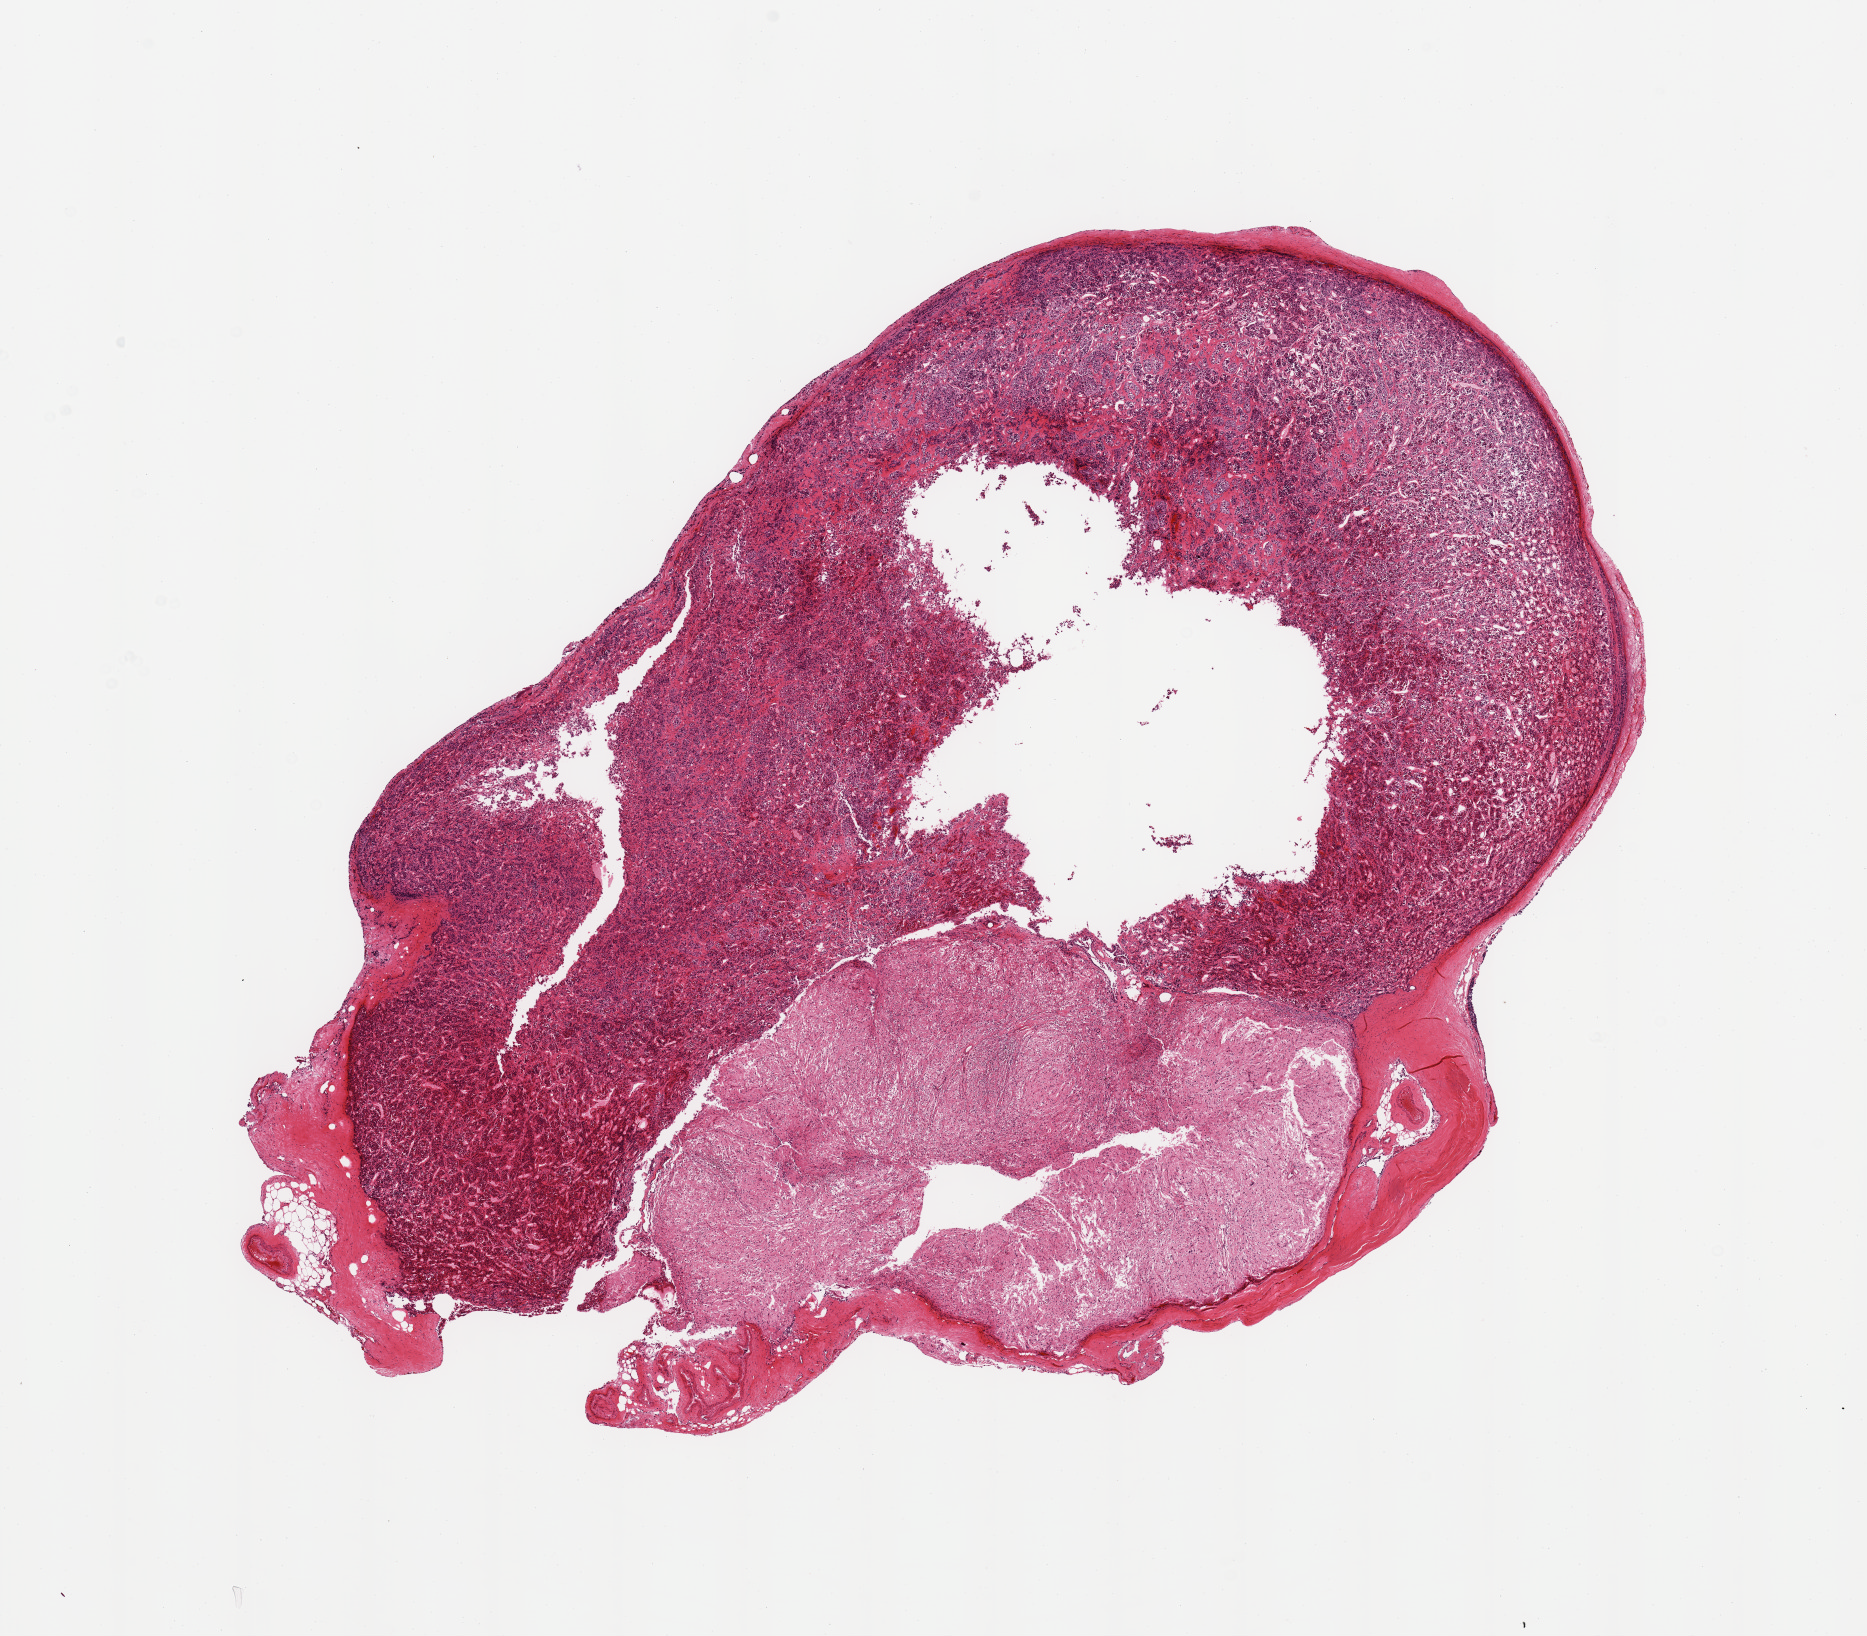
Digitized hematoxylin and eosin (H&E)-stained section, a low-resolution overview of the entire scanned area, about 14.8 x 12.9 mm (from a 20x scan). PAXgene-fixed paraffin-embedded (PFPE) section. Target tissue: pituitary. Donor tissue sample. Male donor.
Pathologist's review note for this sample: 1 piece, ~20% neurohypophysis (, ~5mm focus); rest is adenohypophysis.